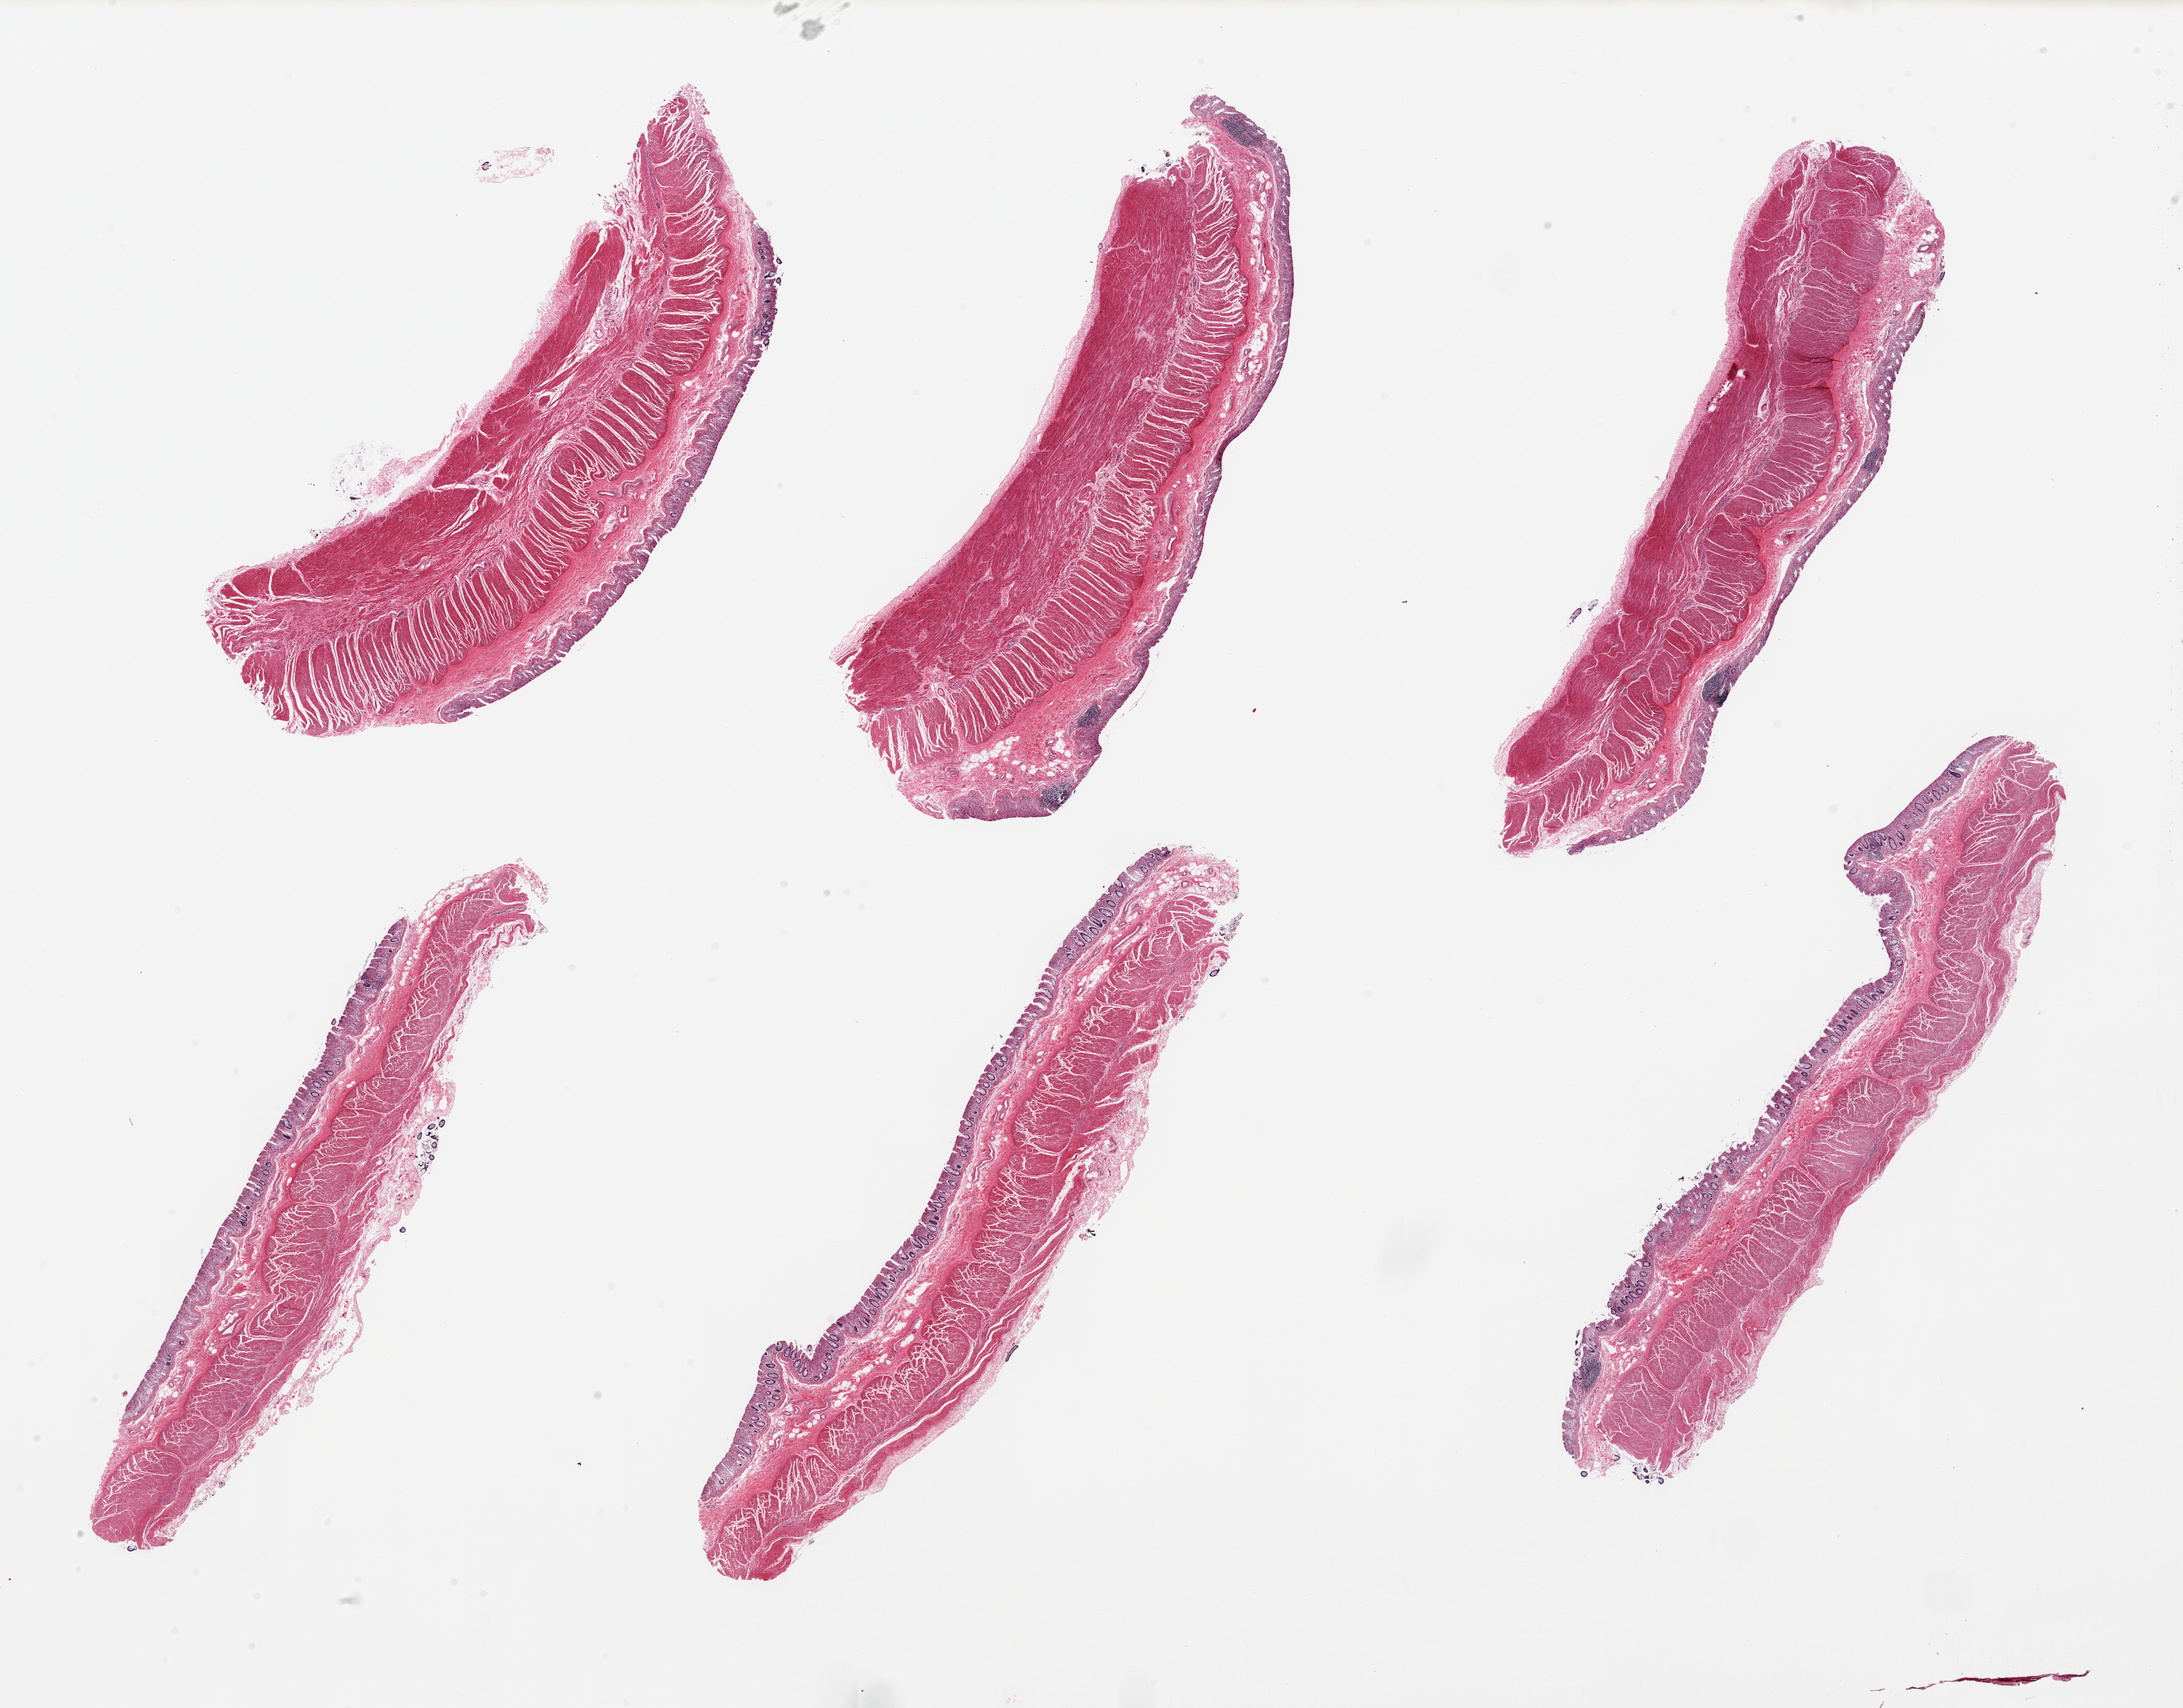
Whole-slide image, haematoxylin and eosin stain, low-resolution overview of the scanned area, about 27.6 x 21.6 mm. Male donor.
Specimen: PAXgene-fixed paraffin-embedded (PFPE) section; target tissue: sigmoid colon; donor tissue sample.